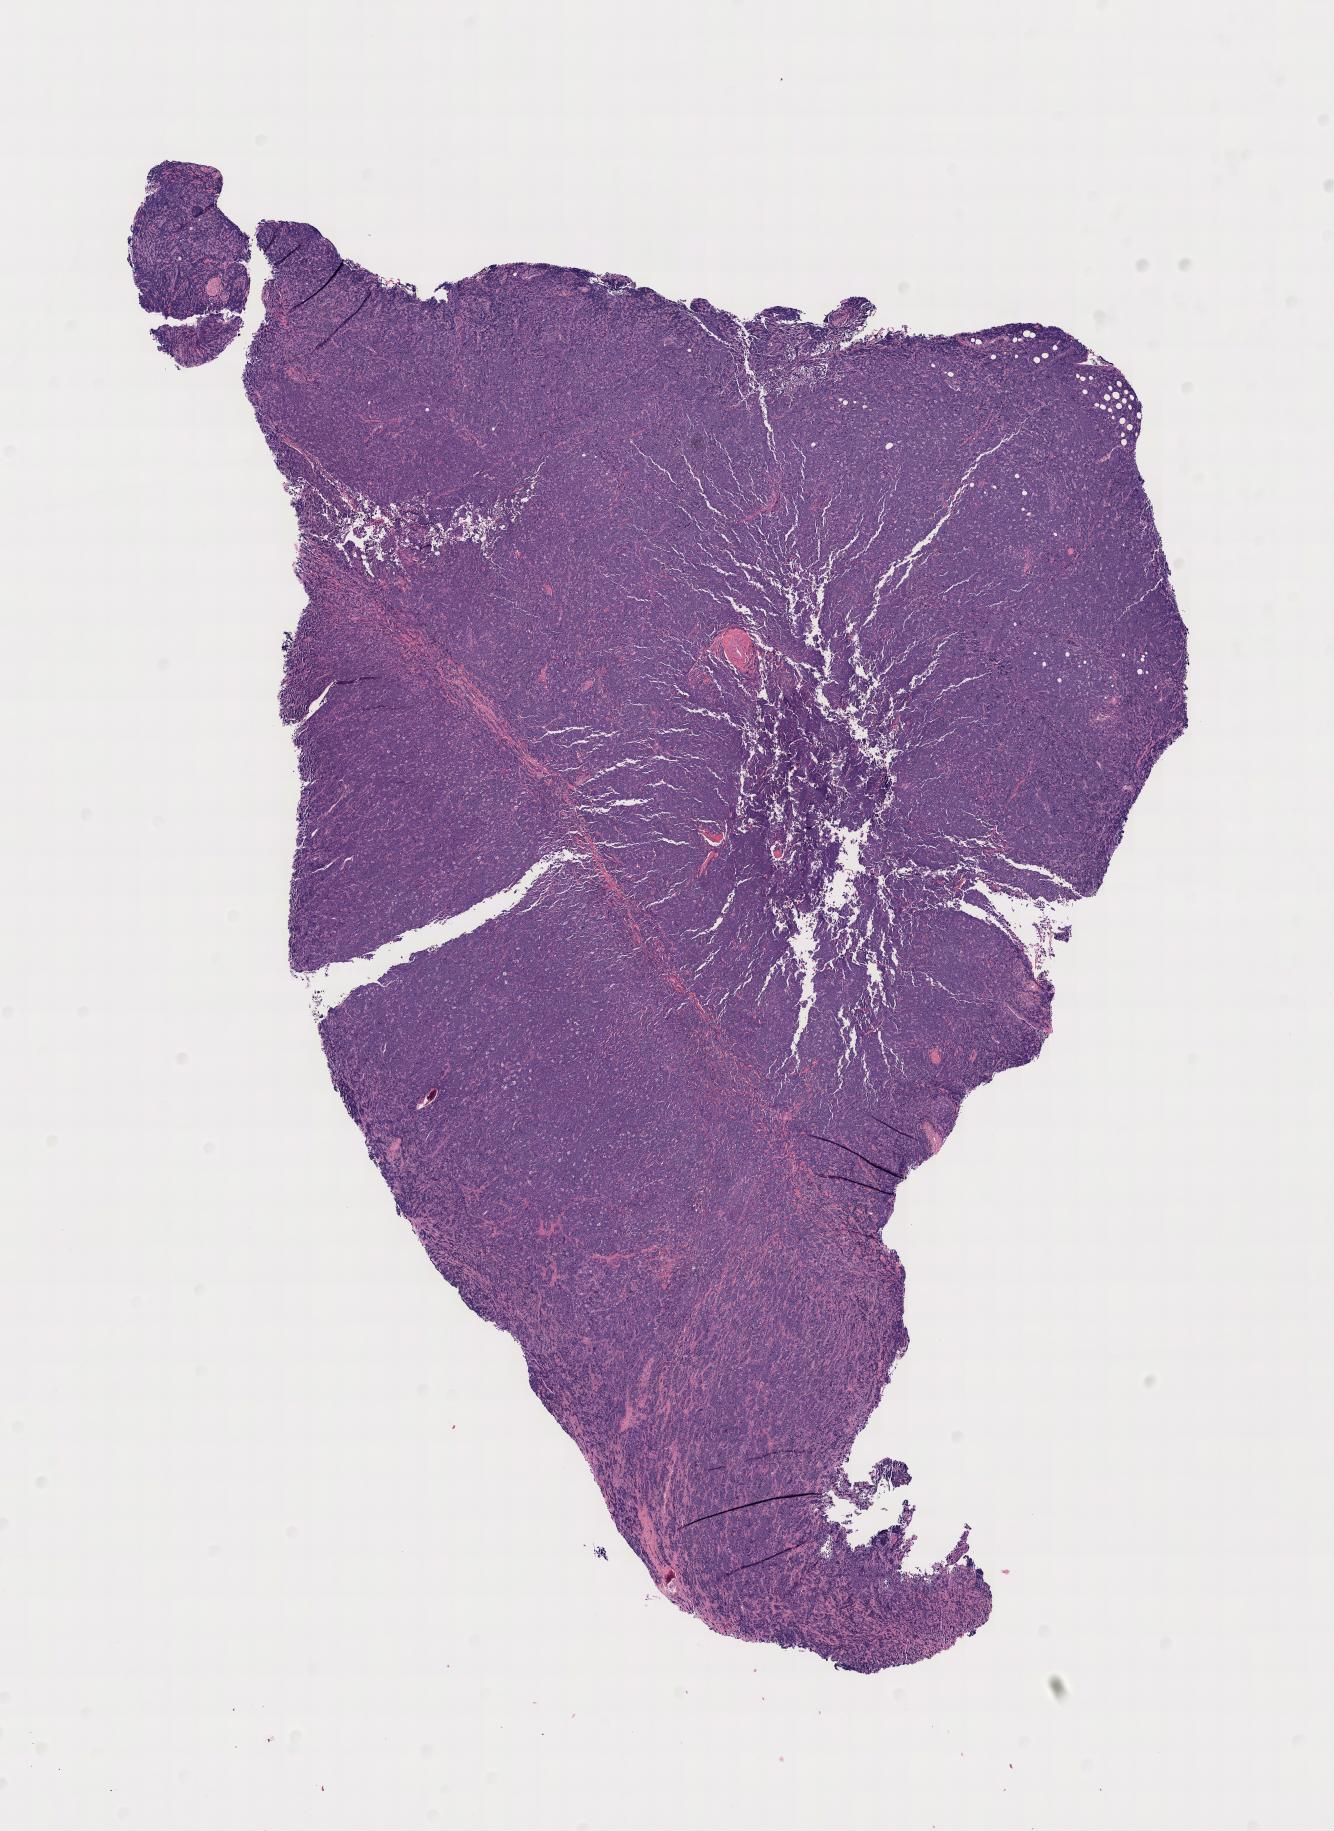
Whole-slide image, hematoxylin and eosin (H&E) stain, a low-resolution overview of the entire scanned area, specimen: tumor tissue, anatomic site: cranium. Patient male; age 11 years.
Diagnosis: Burkitt lymphoma, NOS.